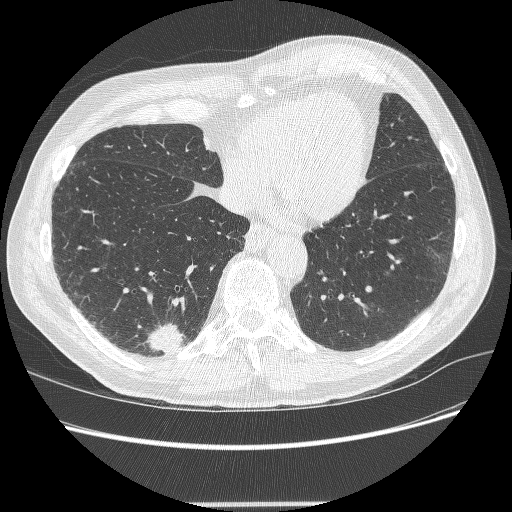
Low-dose screening chest CT, axial slice; second annual screen; lung window (W 1500 / L -600 HU); 1.25 mm slice thickness; slice 70 of 245 in the series; 512 × 512 image matrix, field of view 372 × 372 mm. Male participant, aged 71 years at enrolment.
Expert reader's lesion annotation, bounding box <137,322,189,362> (left, top, right, bottom; pixels). The screening reader recorded 5 non-calcified nodules or masses ≥4 mm on this exam (right lower lobe, right lower lobe, right upper lobe, right upper lobe, right upper lobe); which of them this box marks is not recorded. Lung cancer was diagnosed 7 days after this screen: squamous cell carcinoma, NOS, right lower lobe, moderately differentiated (G2), stage IA (AJCC 6th edition), 27 mm at pathology.